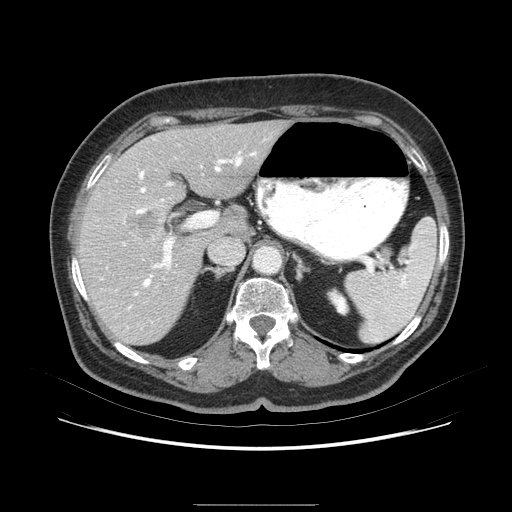
Contrast-enhanced abdominal CT (liver protocol), one axial slice; position 47 of 79 along the scan axis; 120 kVp; soft-tissue window (W 400 / L 40 HU); 2.5 mm slice thickness; 512 × 512 image matrix, field of view 380 × 380 mm. Case-level facts recorded for this patient, not image findings: diagnosis: hepatocellular carcinoma (patient treated with transarterial chemoembolisation; whether this scan precedes or follows treatment is not stated here); TNM stage (as recorded): Stage-I; Child-Pugh class: A; tumour differentiation: poorly differentiated; tumour nodularity: uninodular.
Annotated regions visible in this slice (semi-automatically segmented with operator editing):
- liver parenchyma outside the tumour (the mass and vessels are separate outlines, so this box may not span the whole liver): bounding box <74,124,294,348> (left, top, right, bottom; pixels)
- mass: <131,200,174,234>
- liver vessels: <110,153,255,320>